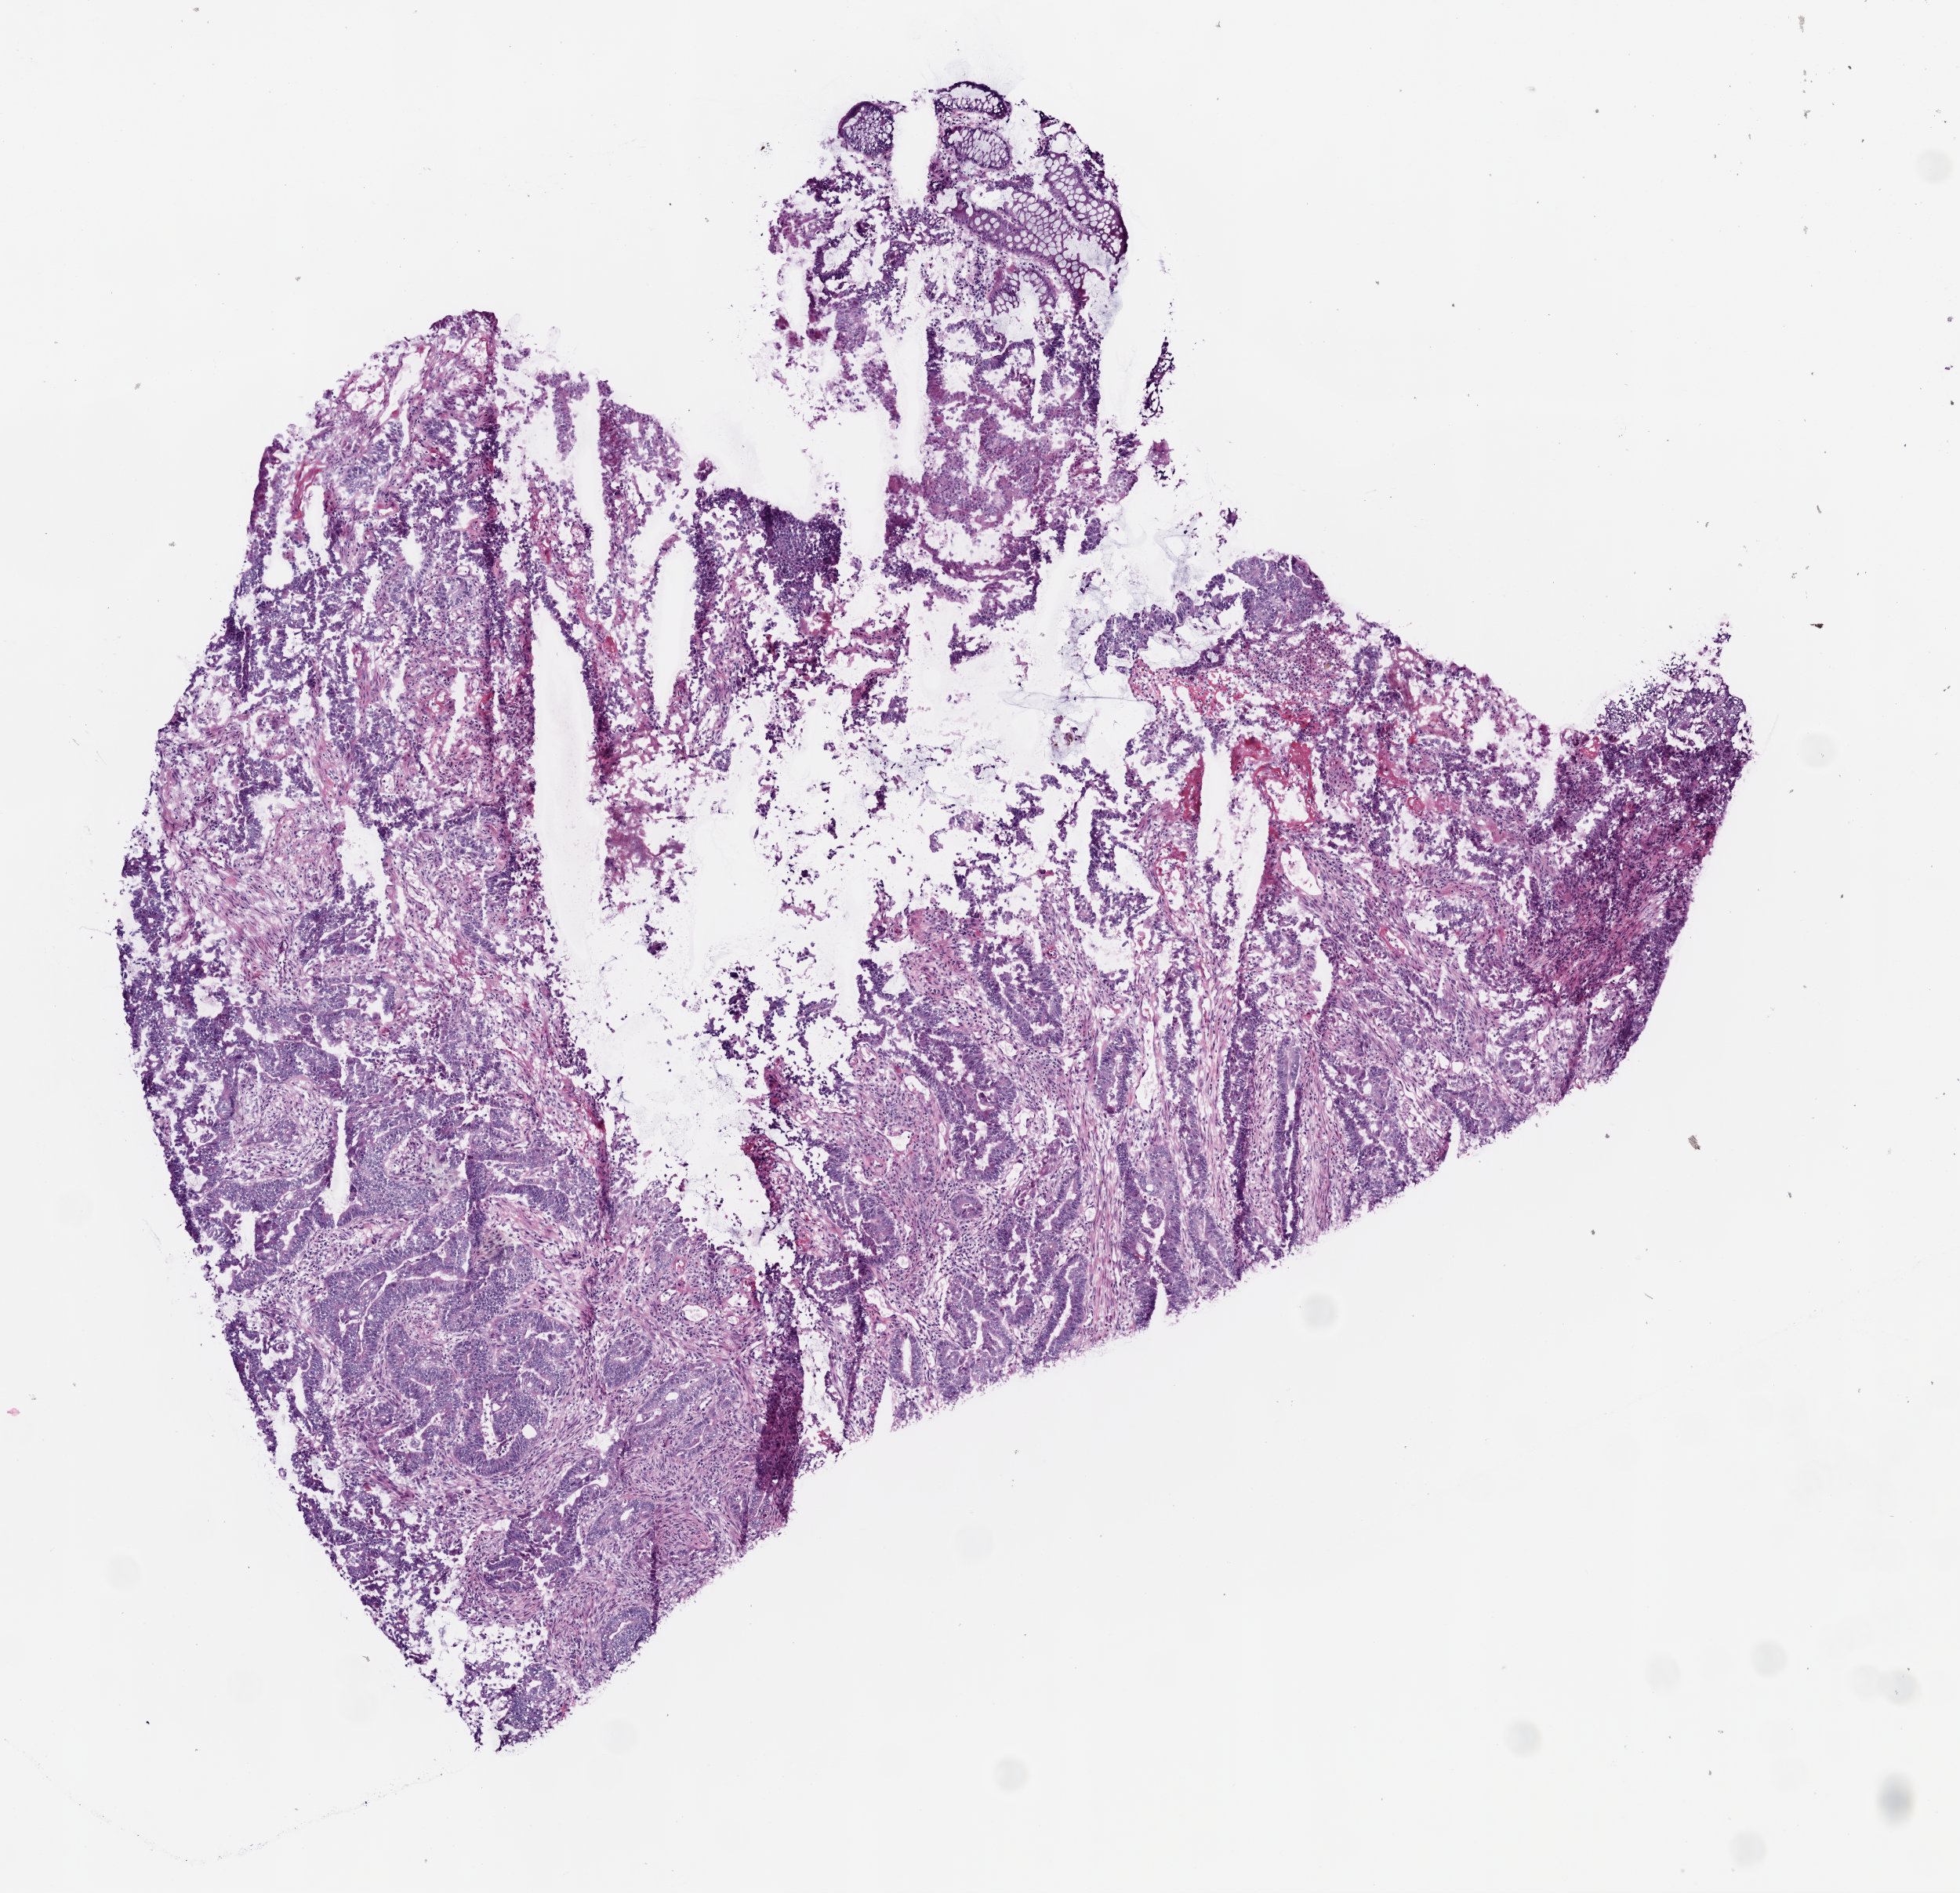
Whole-slide histology image, H&E — shown as a low-resolution overview of the whole scanned area (about 5.0 x 4.8 mm, acquisition: 20x scan). Frozen section. Rectum, primary tumour sample. Patient: female, age at initial diagnosis 66 years. Slide review estimates, as recorded: tumour cells 80%, tumour nuclei 85%.
Pathologic diagnosis: Adenocarcinoma, NOS (rectosigmoid junction).